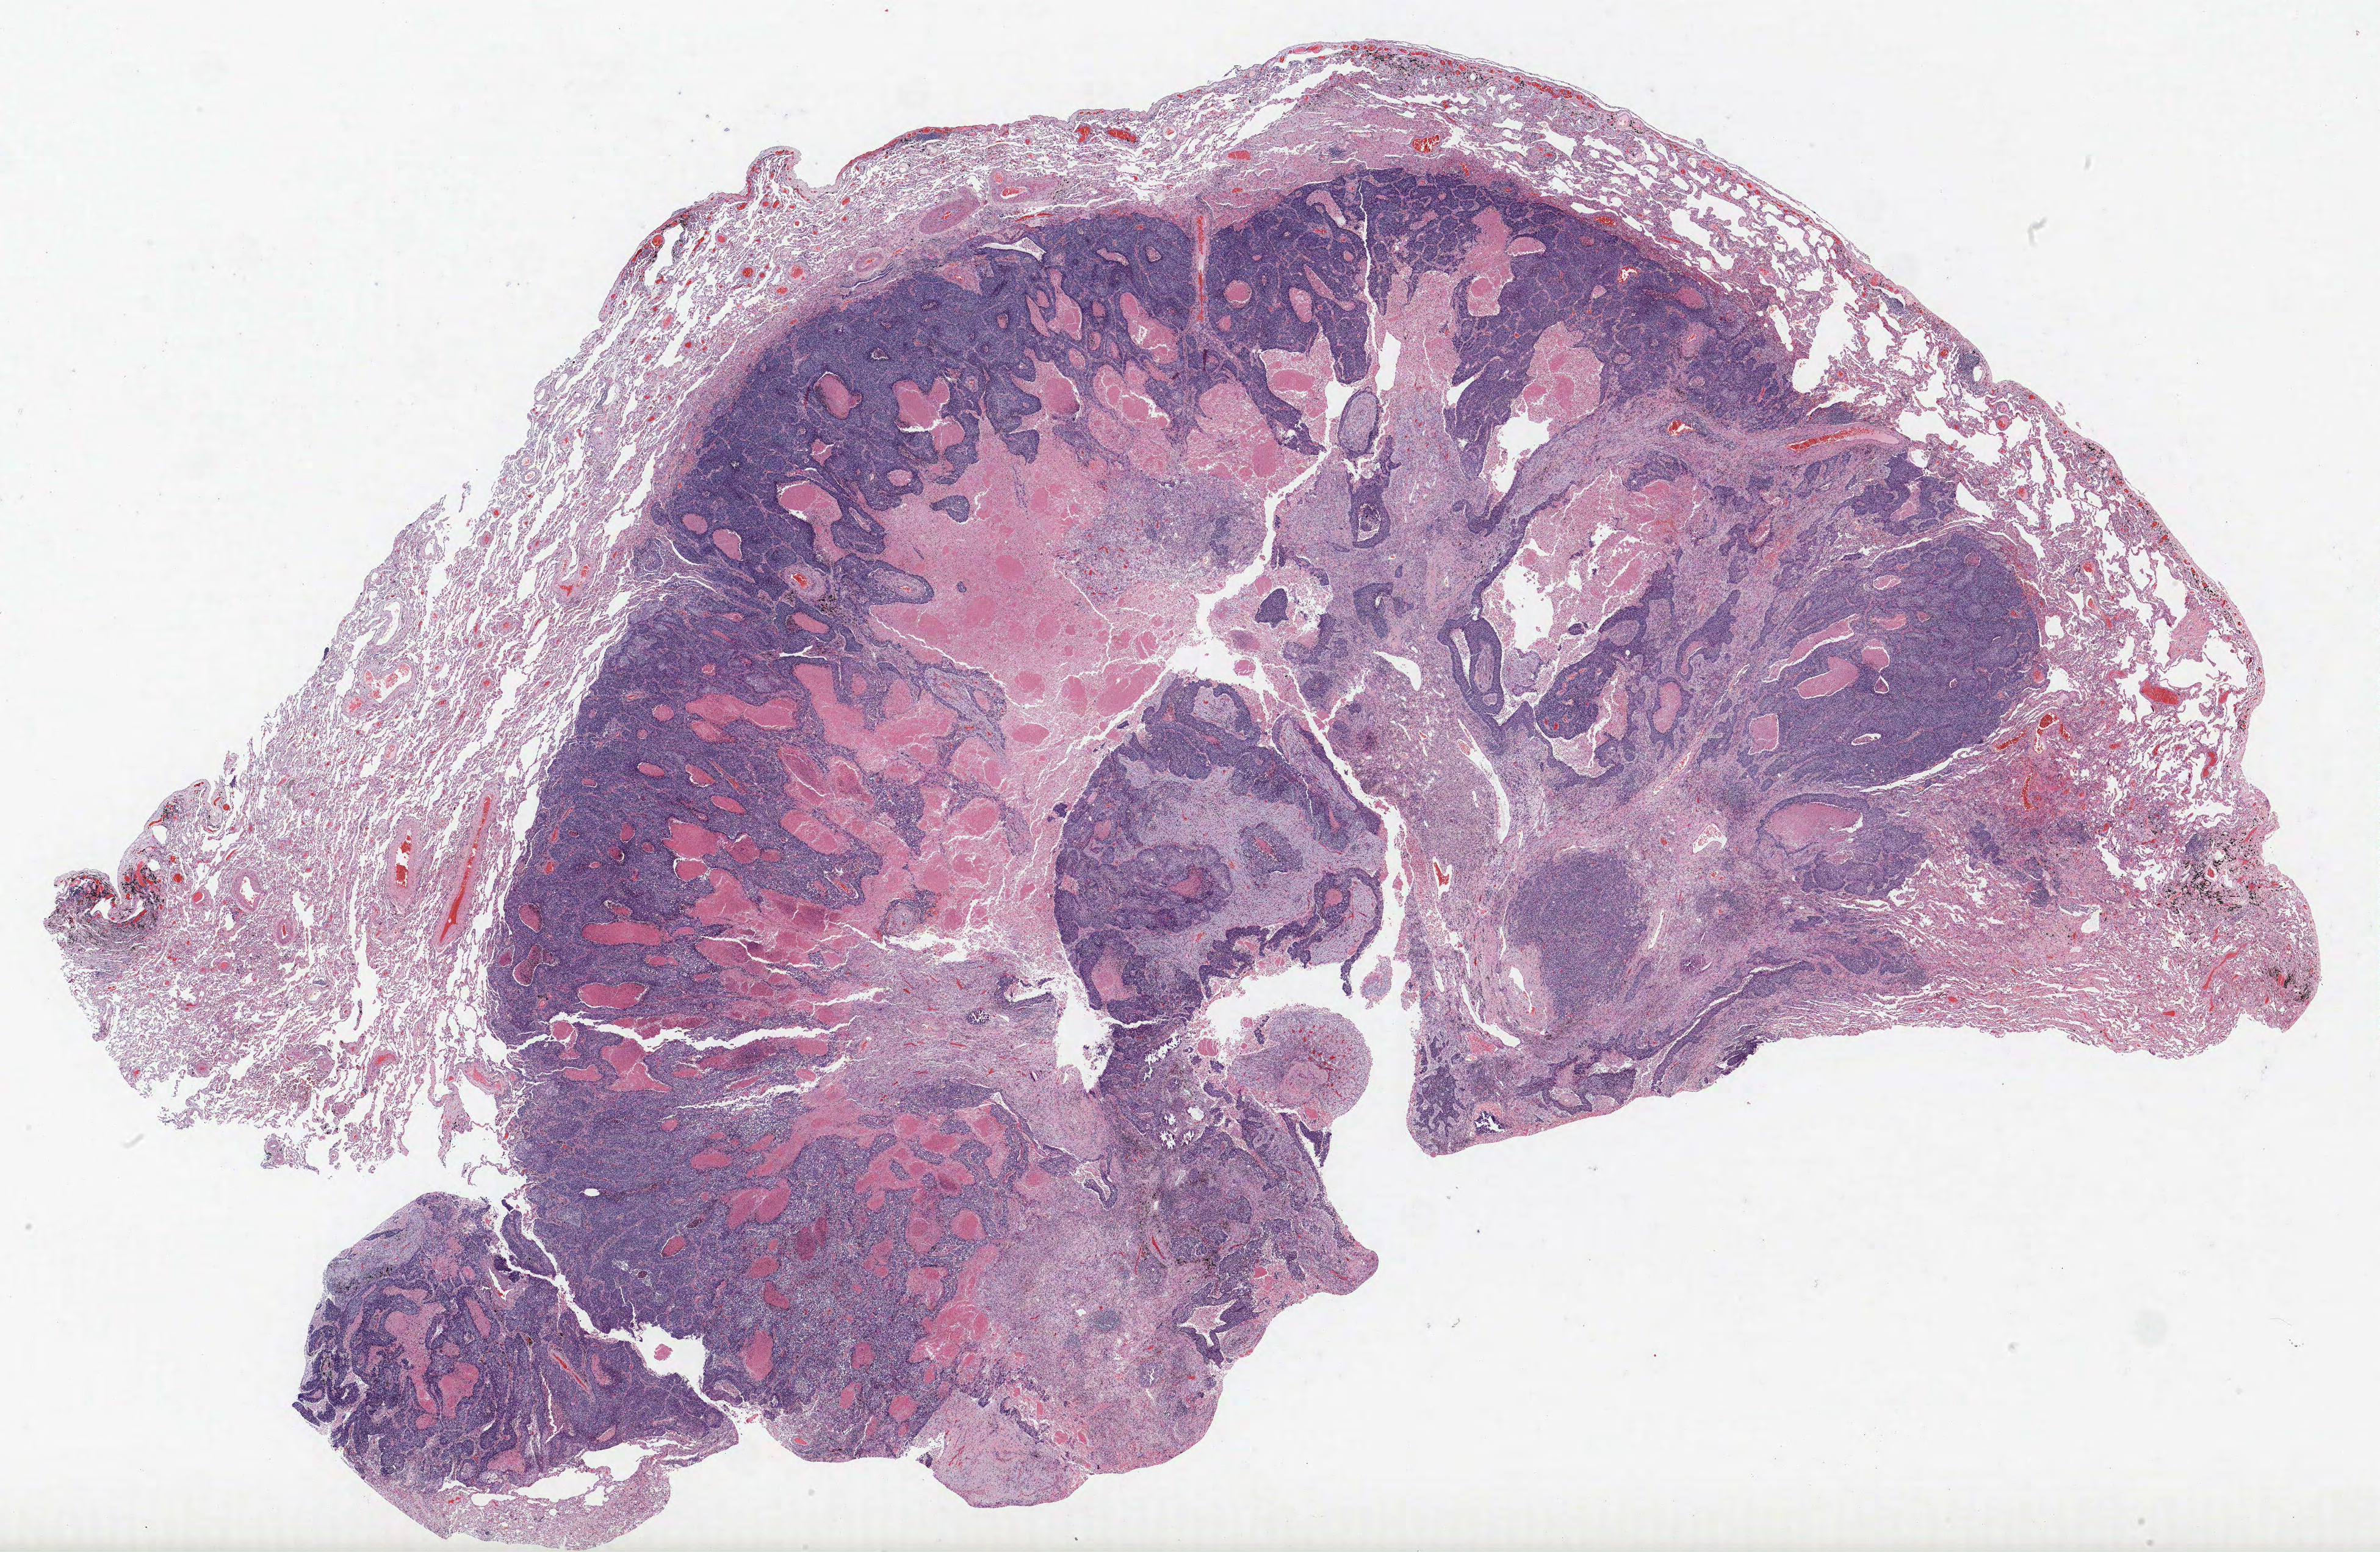
Whole-slide histology image, Hematoxylin and eosin (H&E) stained — a low-resolution overview of the entire scanned area, about 31.2 x 20.4 mm (acquisition: 40x scan), FFPE section, lung tissue. Male, age 66 at enrolment. Current smoker at enrolment. Grade: poorly differentiated (G3).
* primary tumour location (clinical record): left upper lobe
* participant's lung-cancer diagnosis: Squamous cell carcinoma, NOS (ICD-O-3 8070/3)
* stage (AJCC 6th edition): IB
* ICD-O-3 topography: upper lobe of lung (C34.1)
* tumour size (pathology): 30 mm